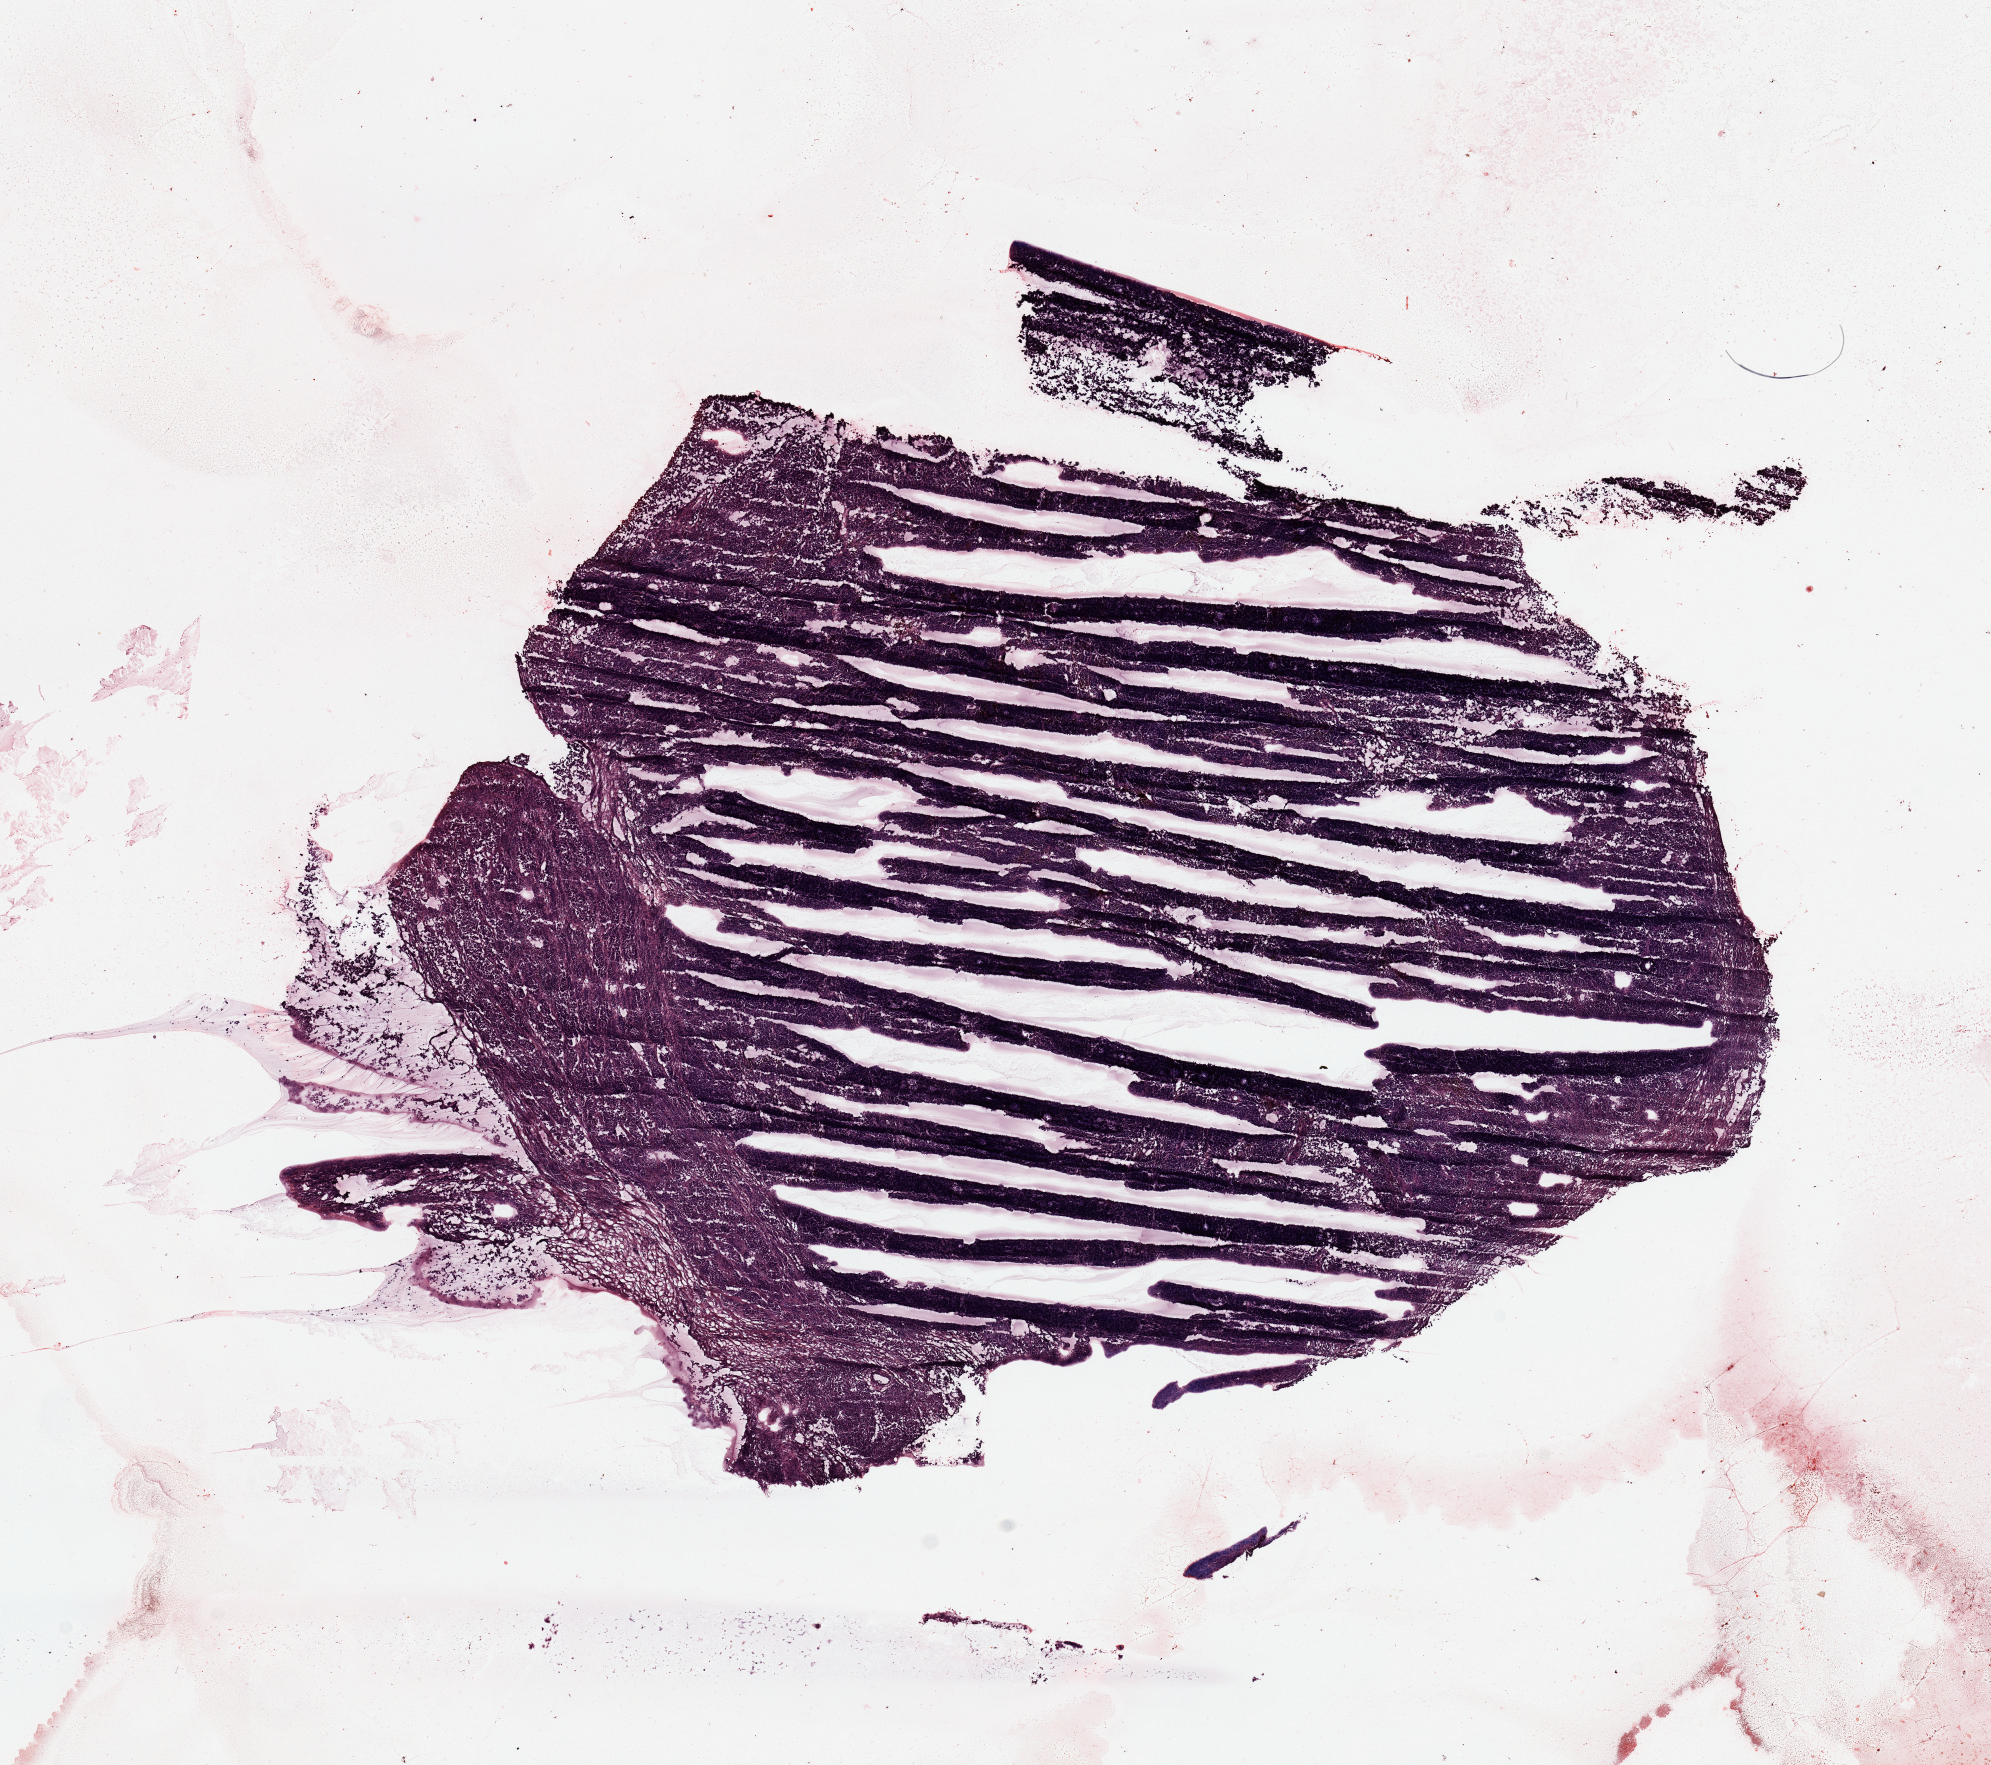
Whole-slide histology image, Hematoxylin and eosin (H&E) stained, low-resolution overview of the scanned area, about 15.8 x 14.0 mm, melanoma tumour tissue; sampled site not recorded. Female, 51 y/o.
Patient diagnosis (cohort enrolment): cutaneous melanoma (skin).